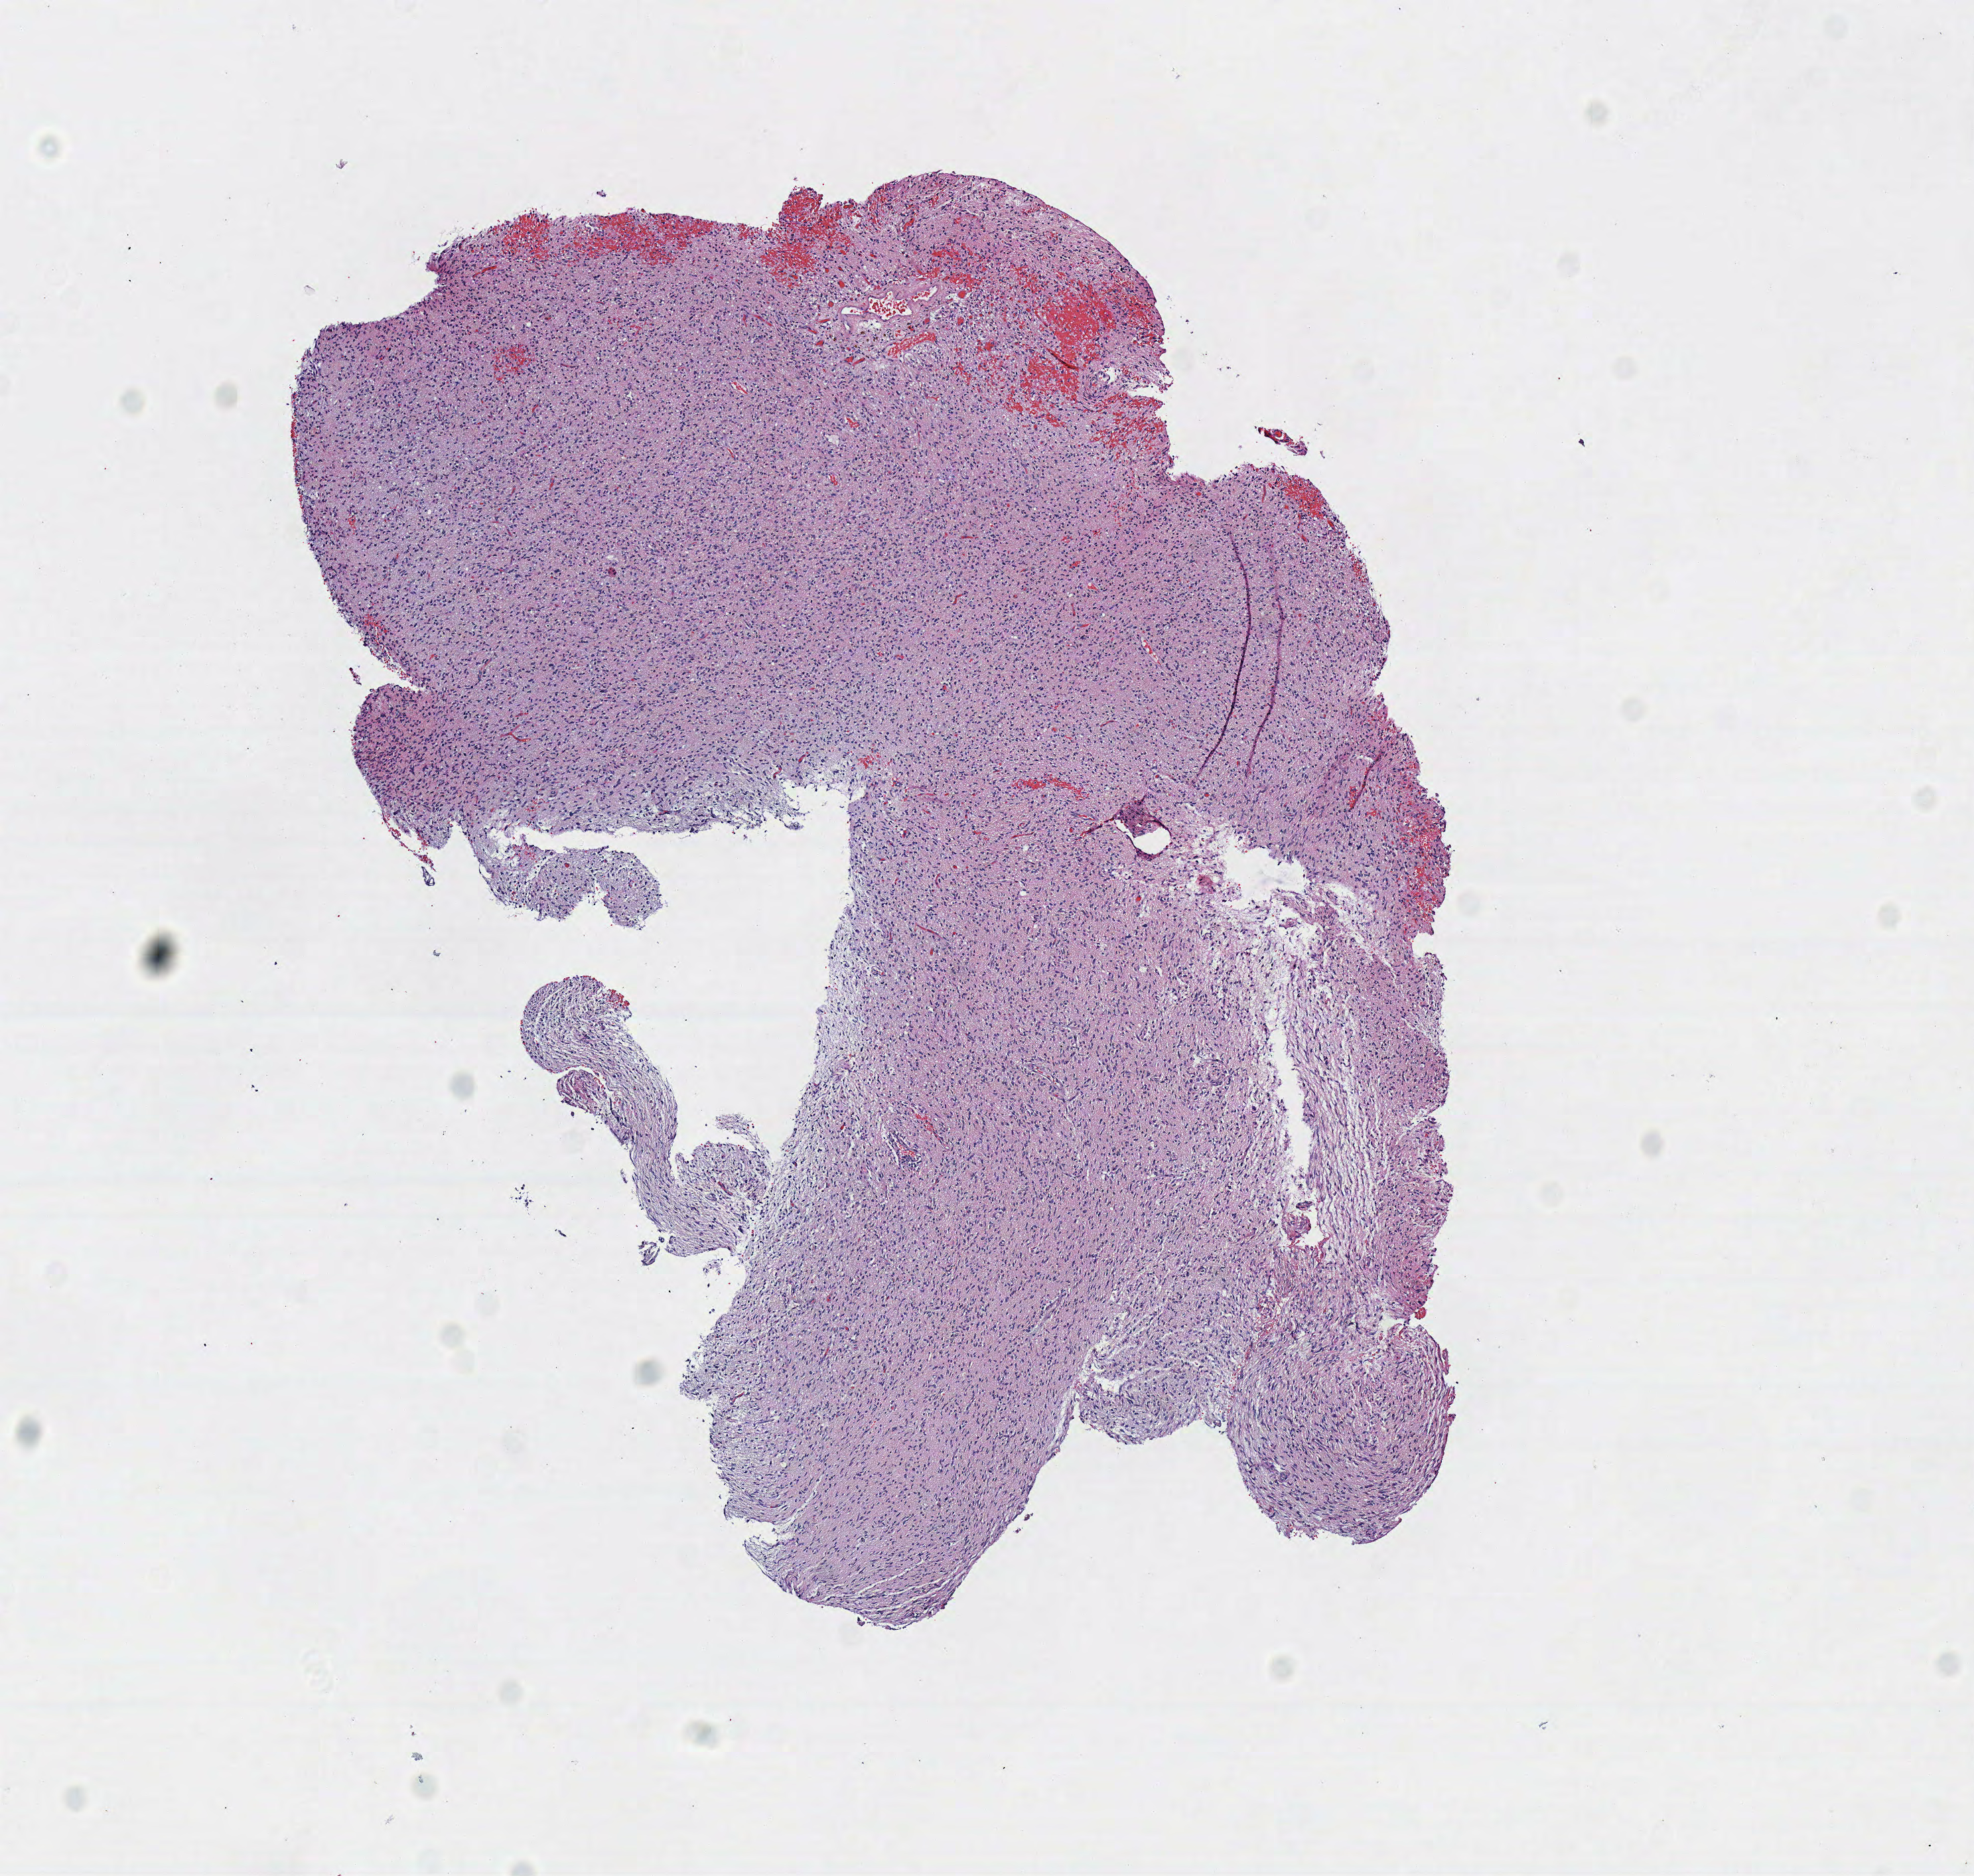
Whole-slide histology image, H&E, a low-resolution overview of the entire scanned area, about 5.9 x 5.6 mm (slide scanned at 40x), frozen section from the top of the tissue portion, primary tumour sample from the brain. Female patient; age at initial diagnosis 57 years. Composition of this section per pathologist review: tumour cells 100%, tumour nuclei 80%.
Diagnosis: Astrocytoma, anaplastic.